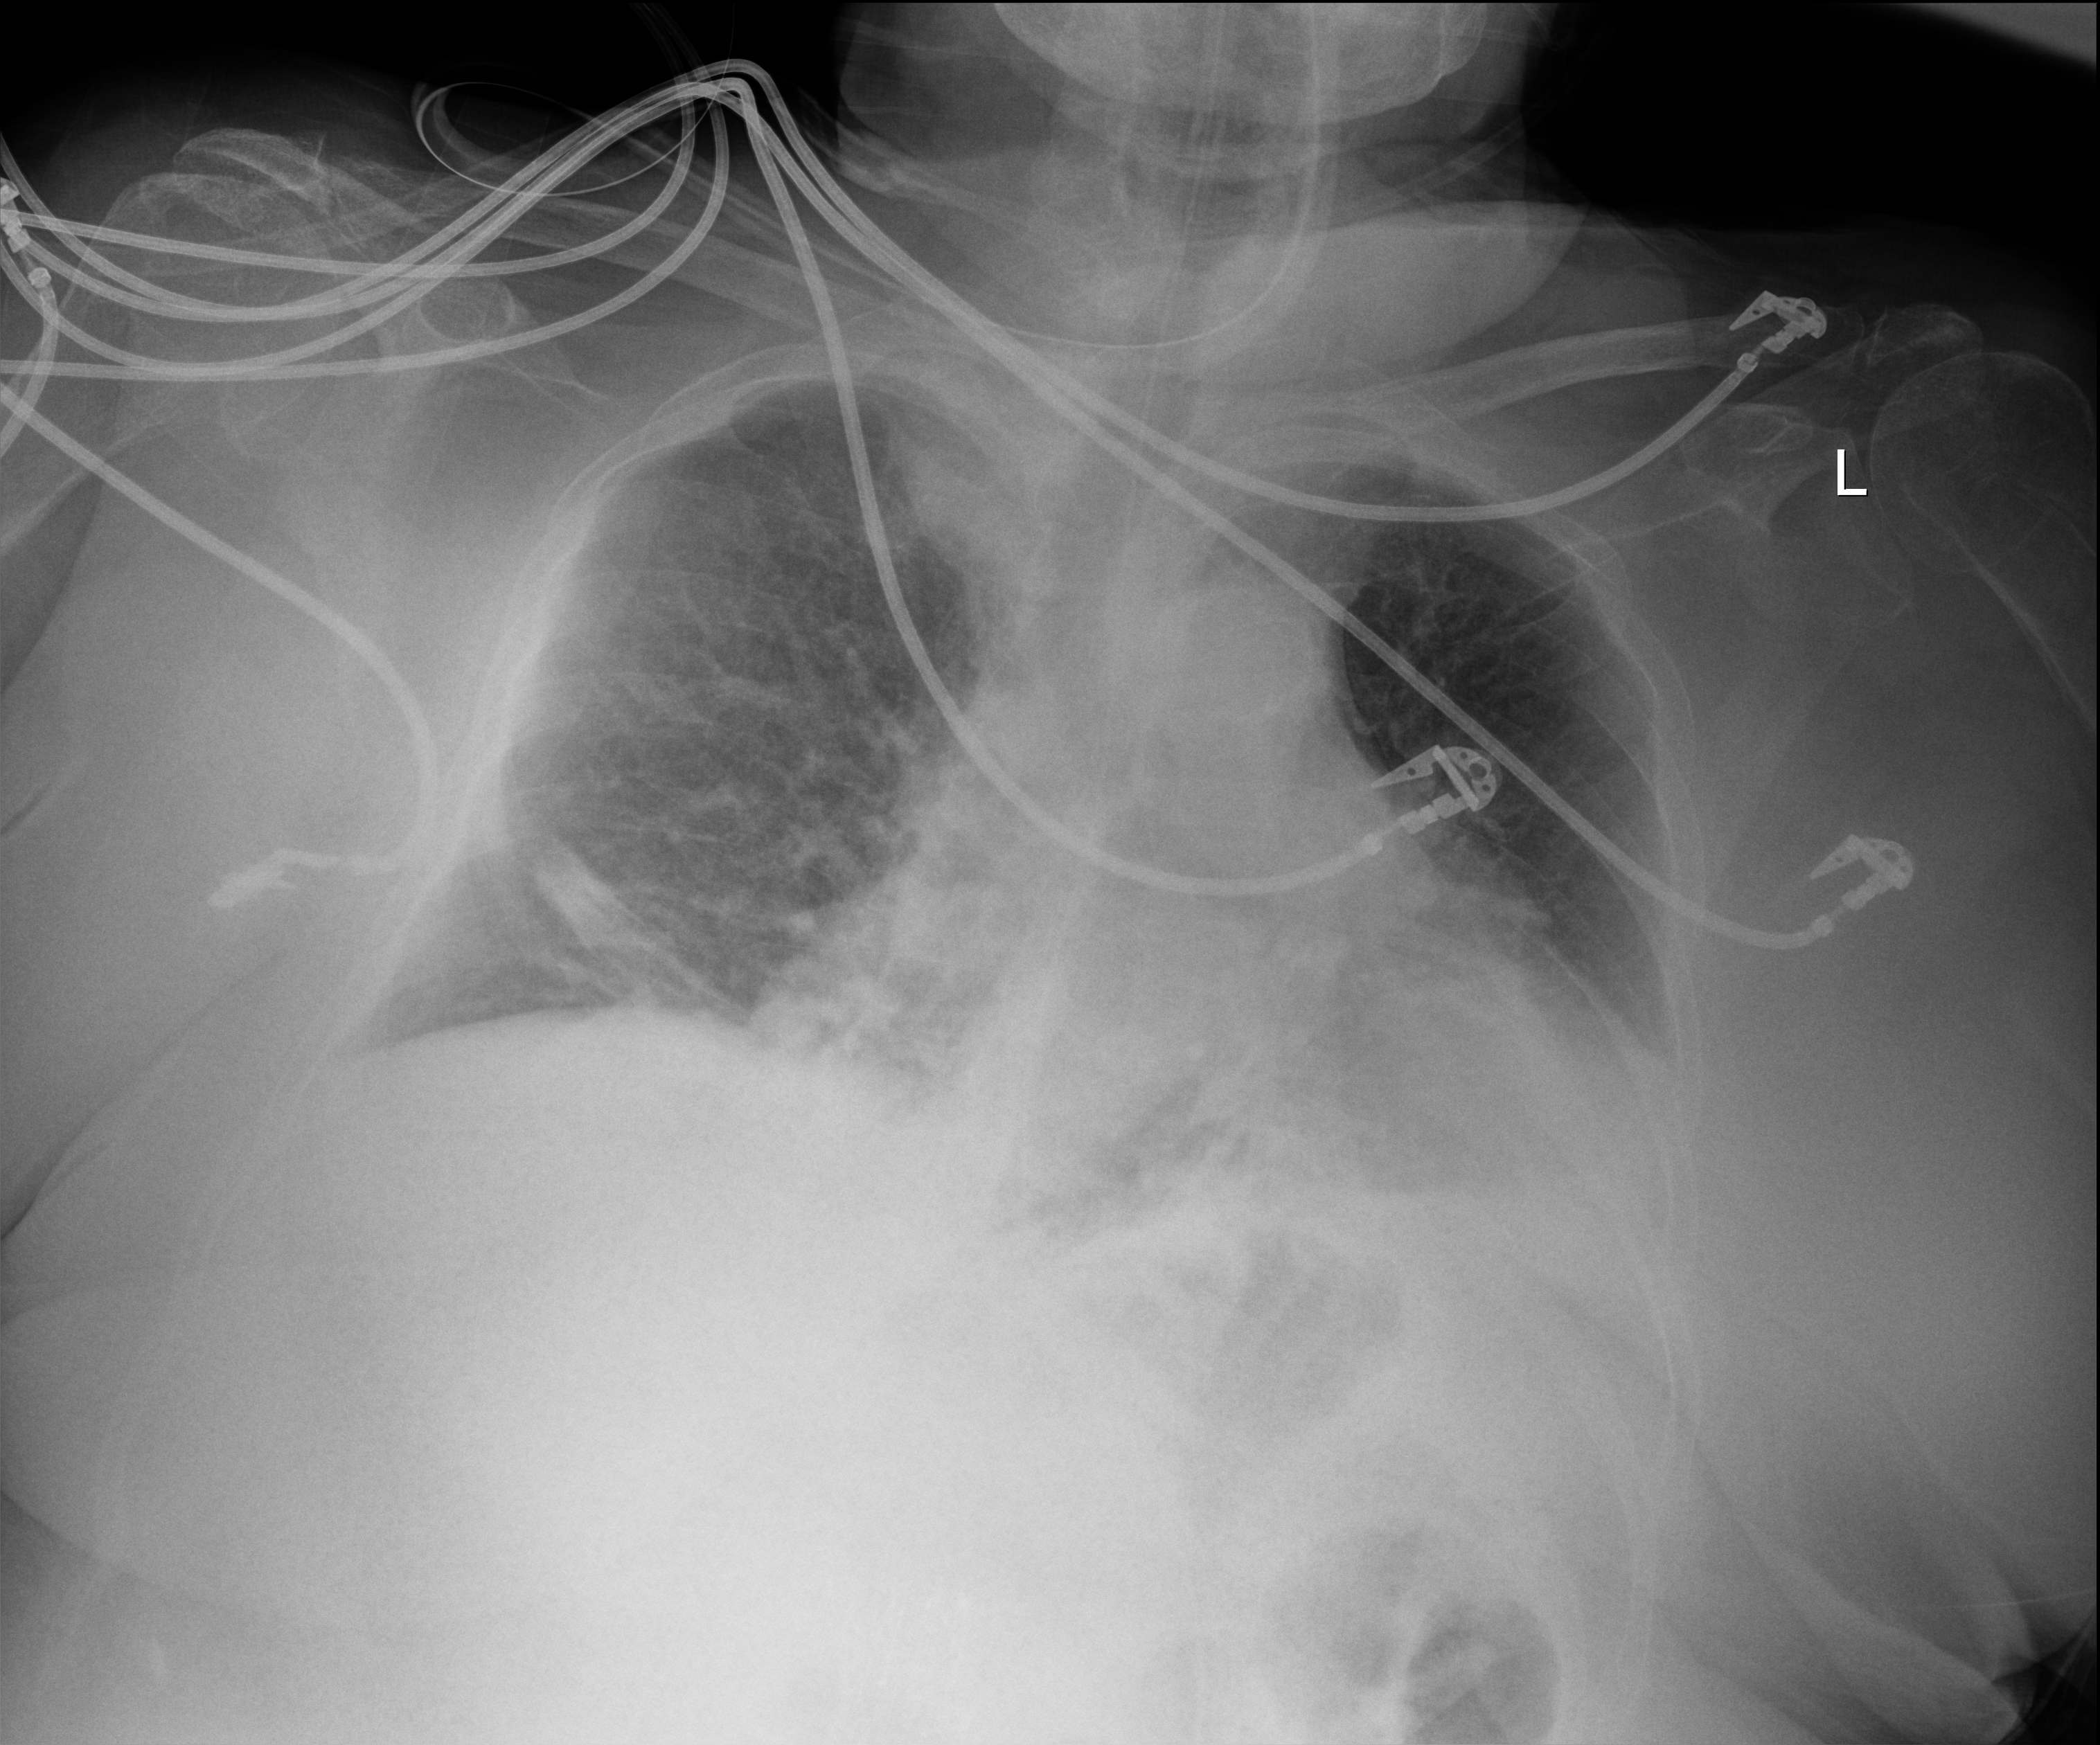
Chest X-ray; anteroposterior (AP) projection. Female patient hospitalised with COVID-19, age 60–74 years.
Admission-level facts for this patient (not findings on this image; timing relative to this image not recorded):
- admitted to intensive care during this hospital stay: yes
- mechanically ventilated during this hospital stay: no